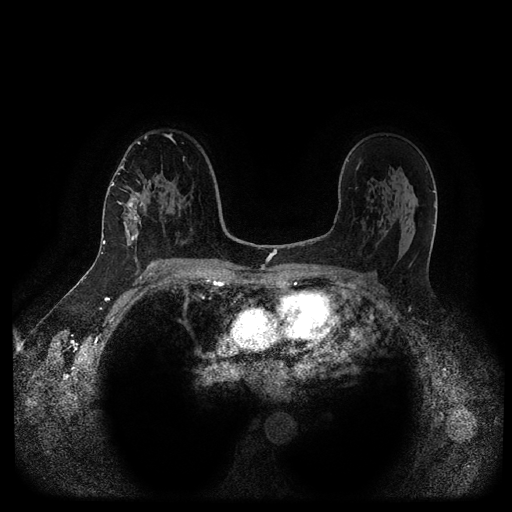
Breast MRI (dynamic contrast-enhanced, multi-phase), one axial slice. Slice 63 of 116 in the series (ordered by position). Dynamic contrast-enhanced series, time point 2 of 5 at this slice position (early post-contrast). 1.5 T. TE 2.6 ms, TR 5.3 ms. 512 × 512 image matrix. Female patient, age 58 years.
Annotated regions visible in this slice (semi-automatically segmented with operator editing):
- breast lesion (labelled 'tumour' in the annotation; benign lesions carry a separate 'benign' label): bounding box <121,193,145,252> (left, top, right, bottom; pixels)